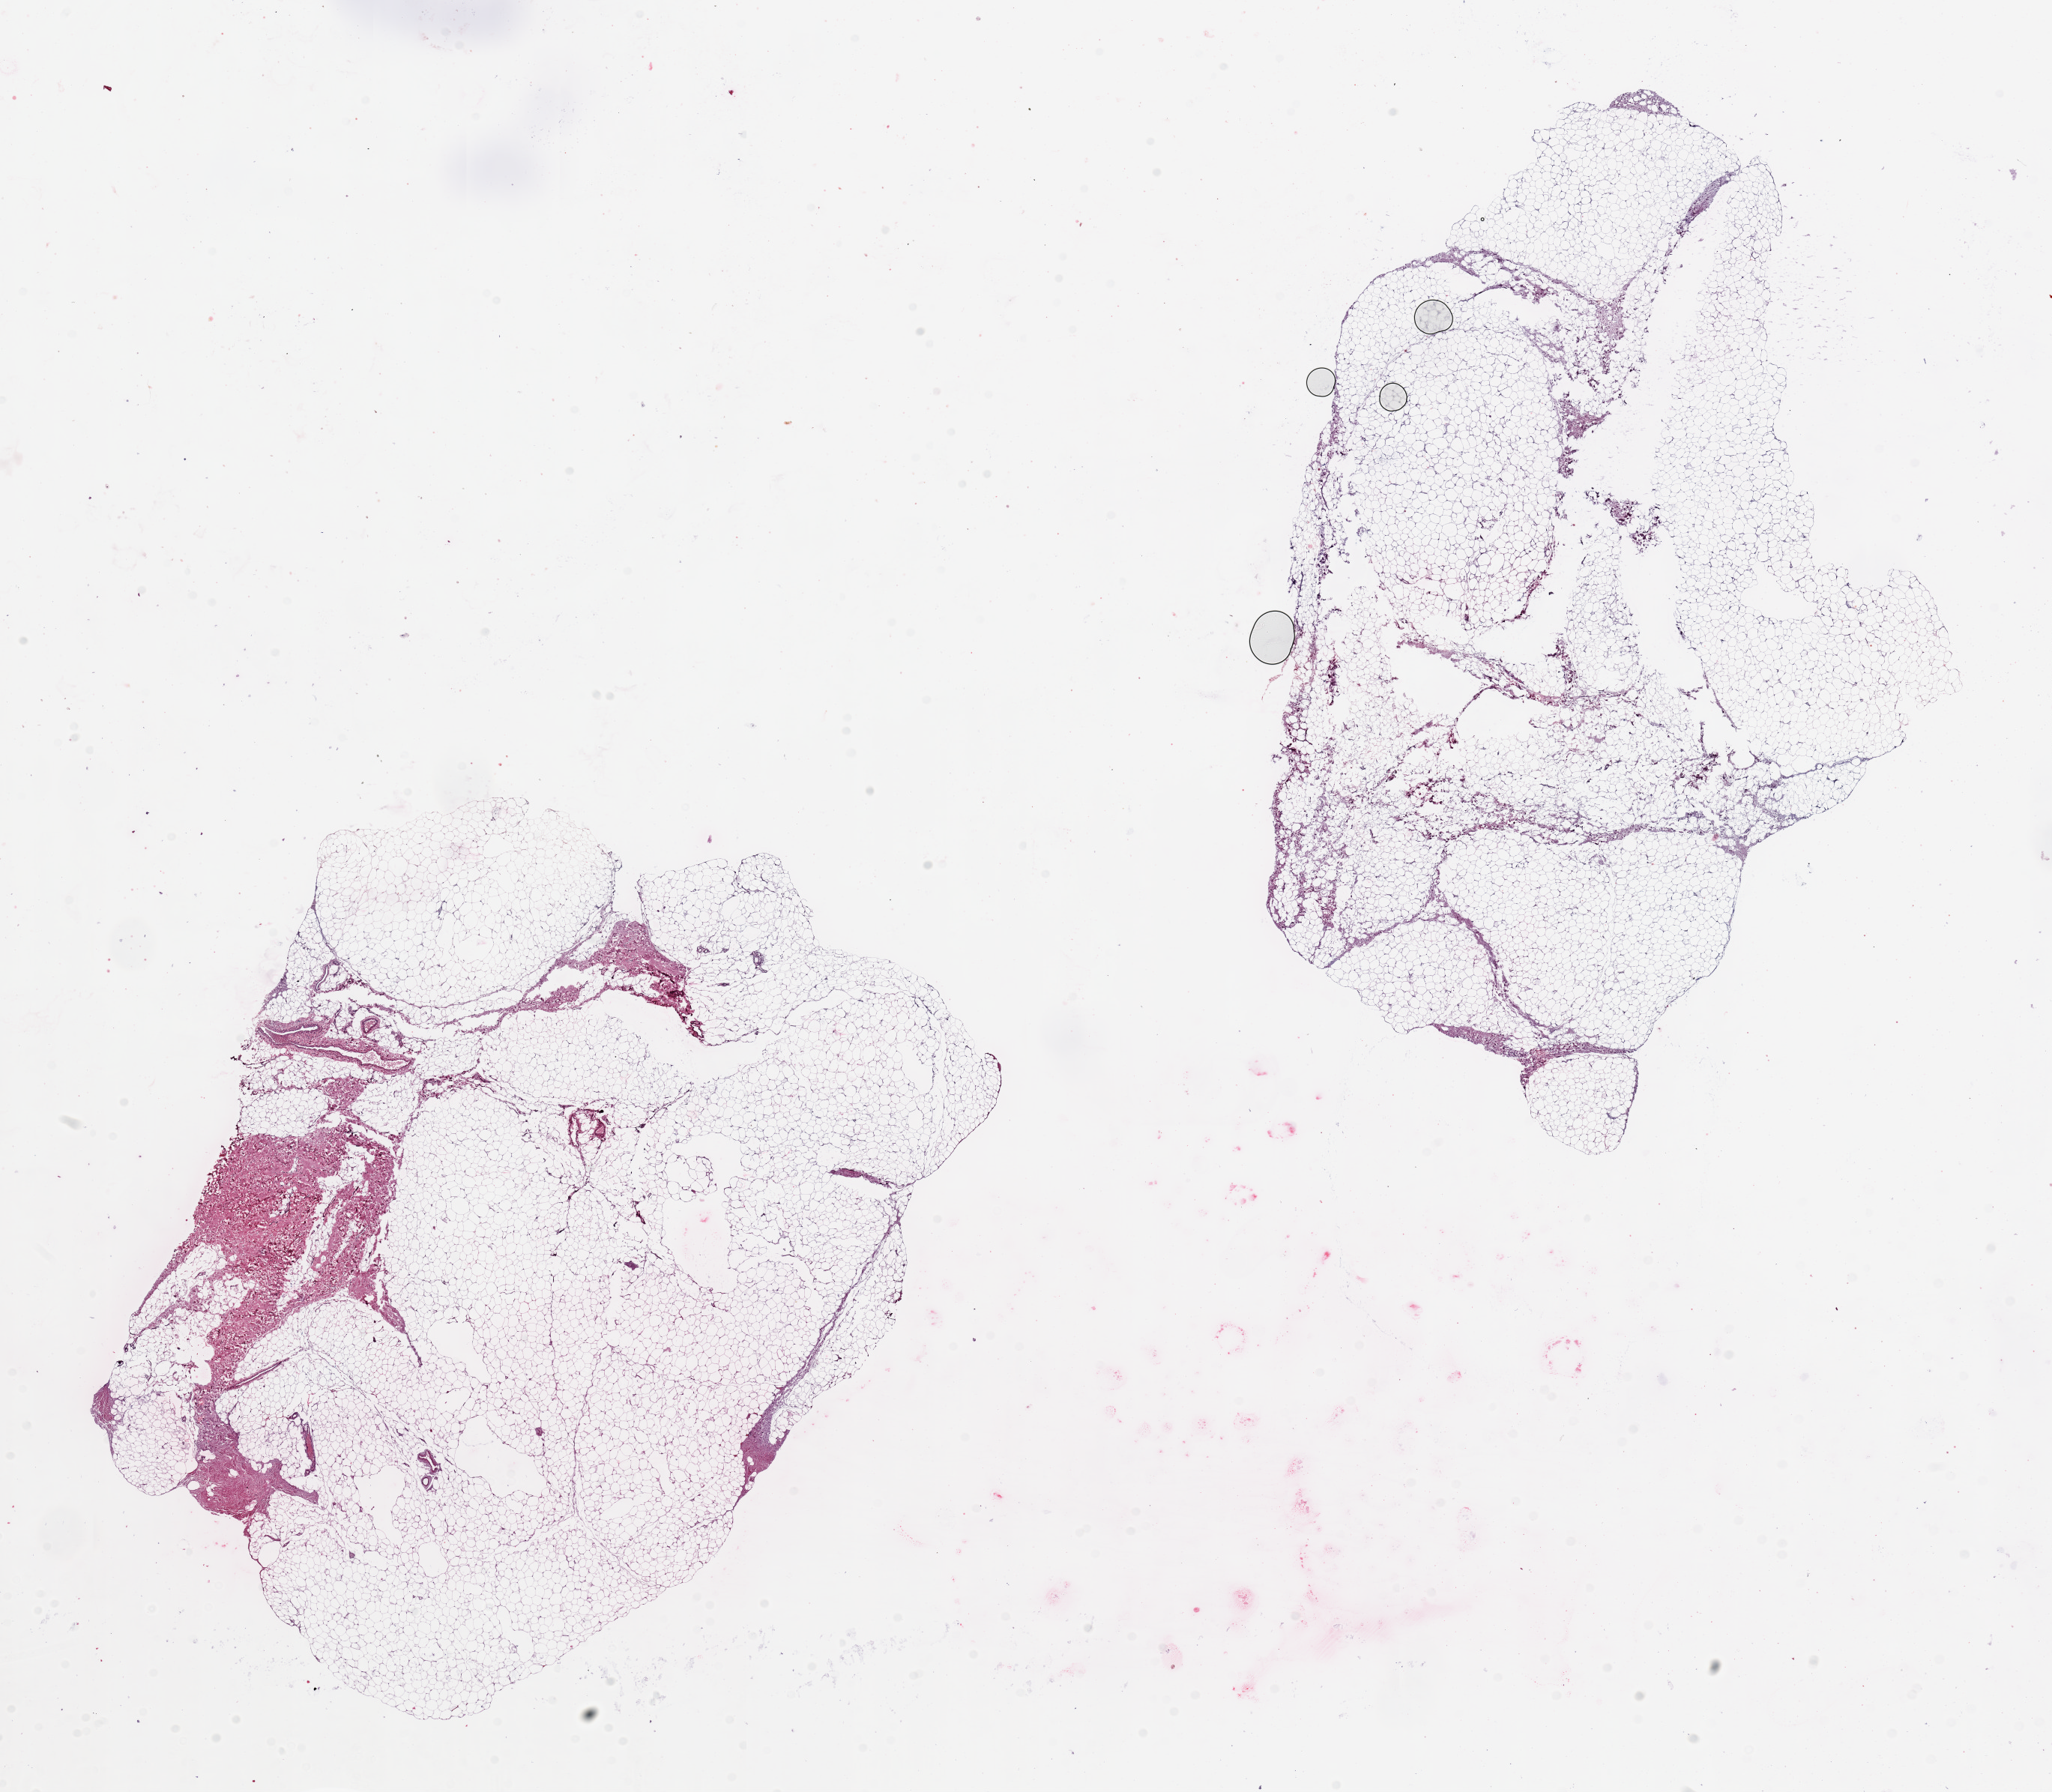
Digitized haematoxylin and eosin-stained section — shown as a low-resolution overview of the whole scanned area (about 21.7 x 18.9 mm, slide scanned at 20x). PAXgene-fixed paraffin-embedded (PFPE) section. Target tissue: breast. Tissue donor sample. Male donor.
Reviewer comment on this tissue sample: 2 pieces. 10x8 & 11x7mm; mainly fat, focal fibrous areas, no ductal elements noted.